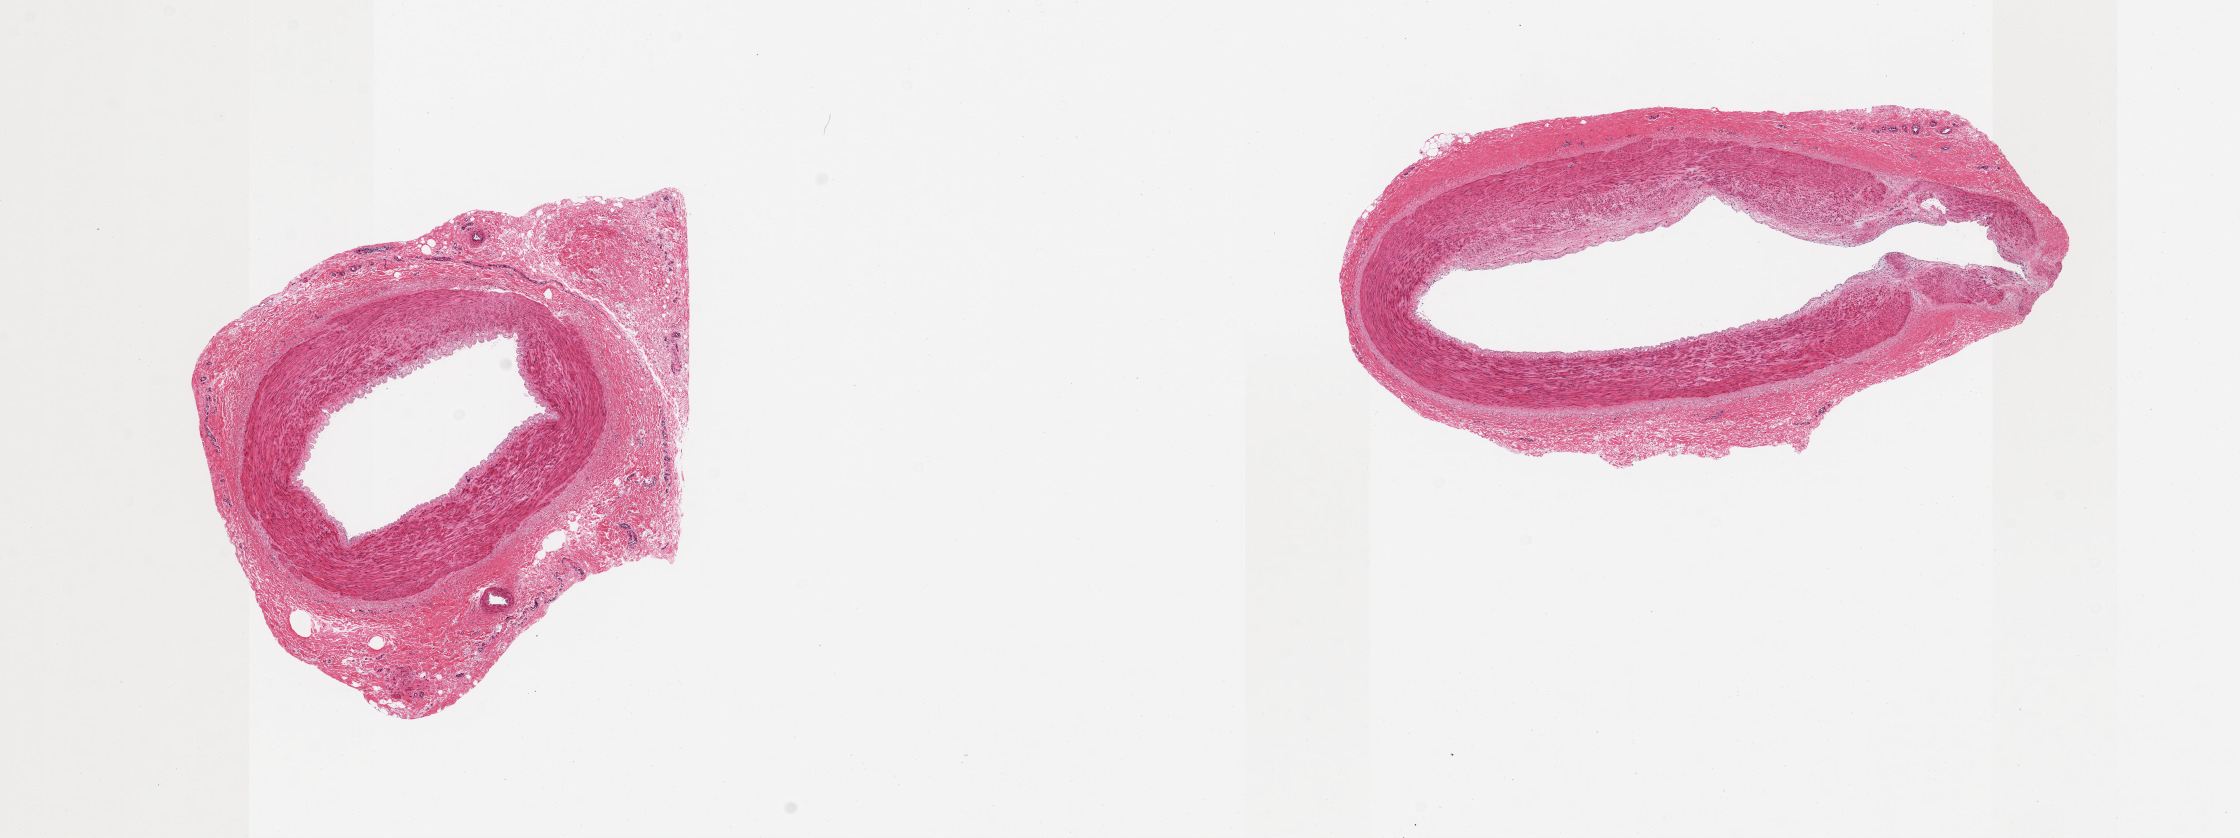
H&E whole-slide image — low-resolution overview of the scanned area, about 17.7 x 6.6 mm (from a 20x scan), PAXgene-fixed, paraffin-embedded tissue, sampled site (target tissue): tibial artery, tissue donor sample. Donor: female.
• reviewer comment on this tissue sample: 1 piece; artery not nerve; well trimmed